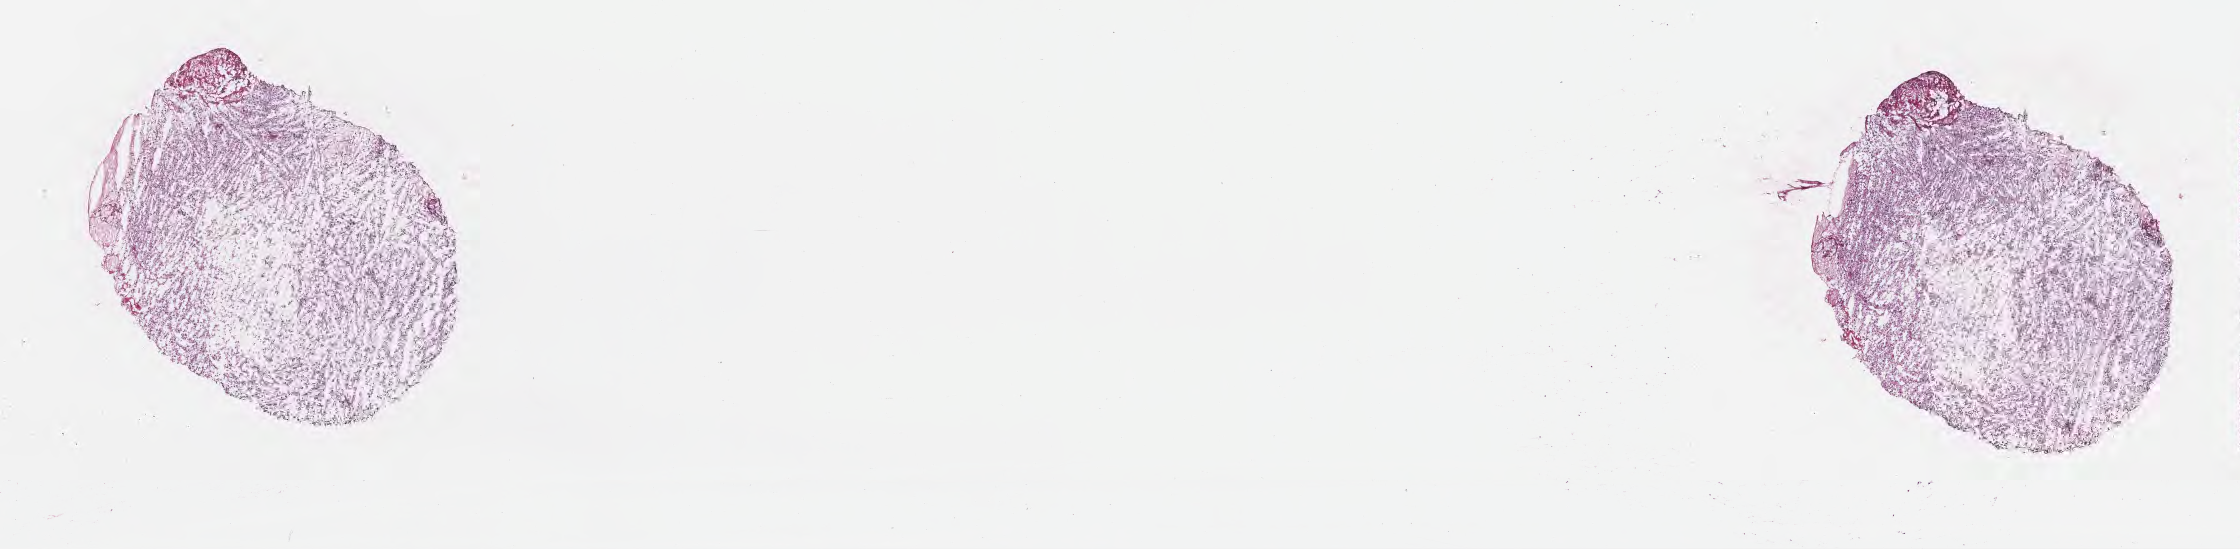
Hematoxylin and eosin (H&E) whole-slide image, shown as a low-resolution overview of the whole scanned area (about 18.1 x 4.4 mm), frozen section, recurrent tumor, site: brain. Male patient; age at initial diagnosis 63 years. Slide review estimates, as recorded: tumor cells 77%, tumor nuclei 88%, stromal cells 7%, necrosis 5%, normal cells 11%. Infiltration values recorded for this section: lymphocyte infiltration 0%, monocyte infiltration 0%, neutrophil infiltration 0%.
Section: top of the tissue portion. Patient diagnosis: Glioblastoma, NOS.